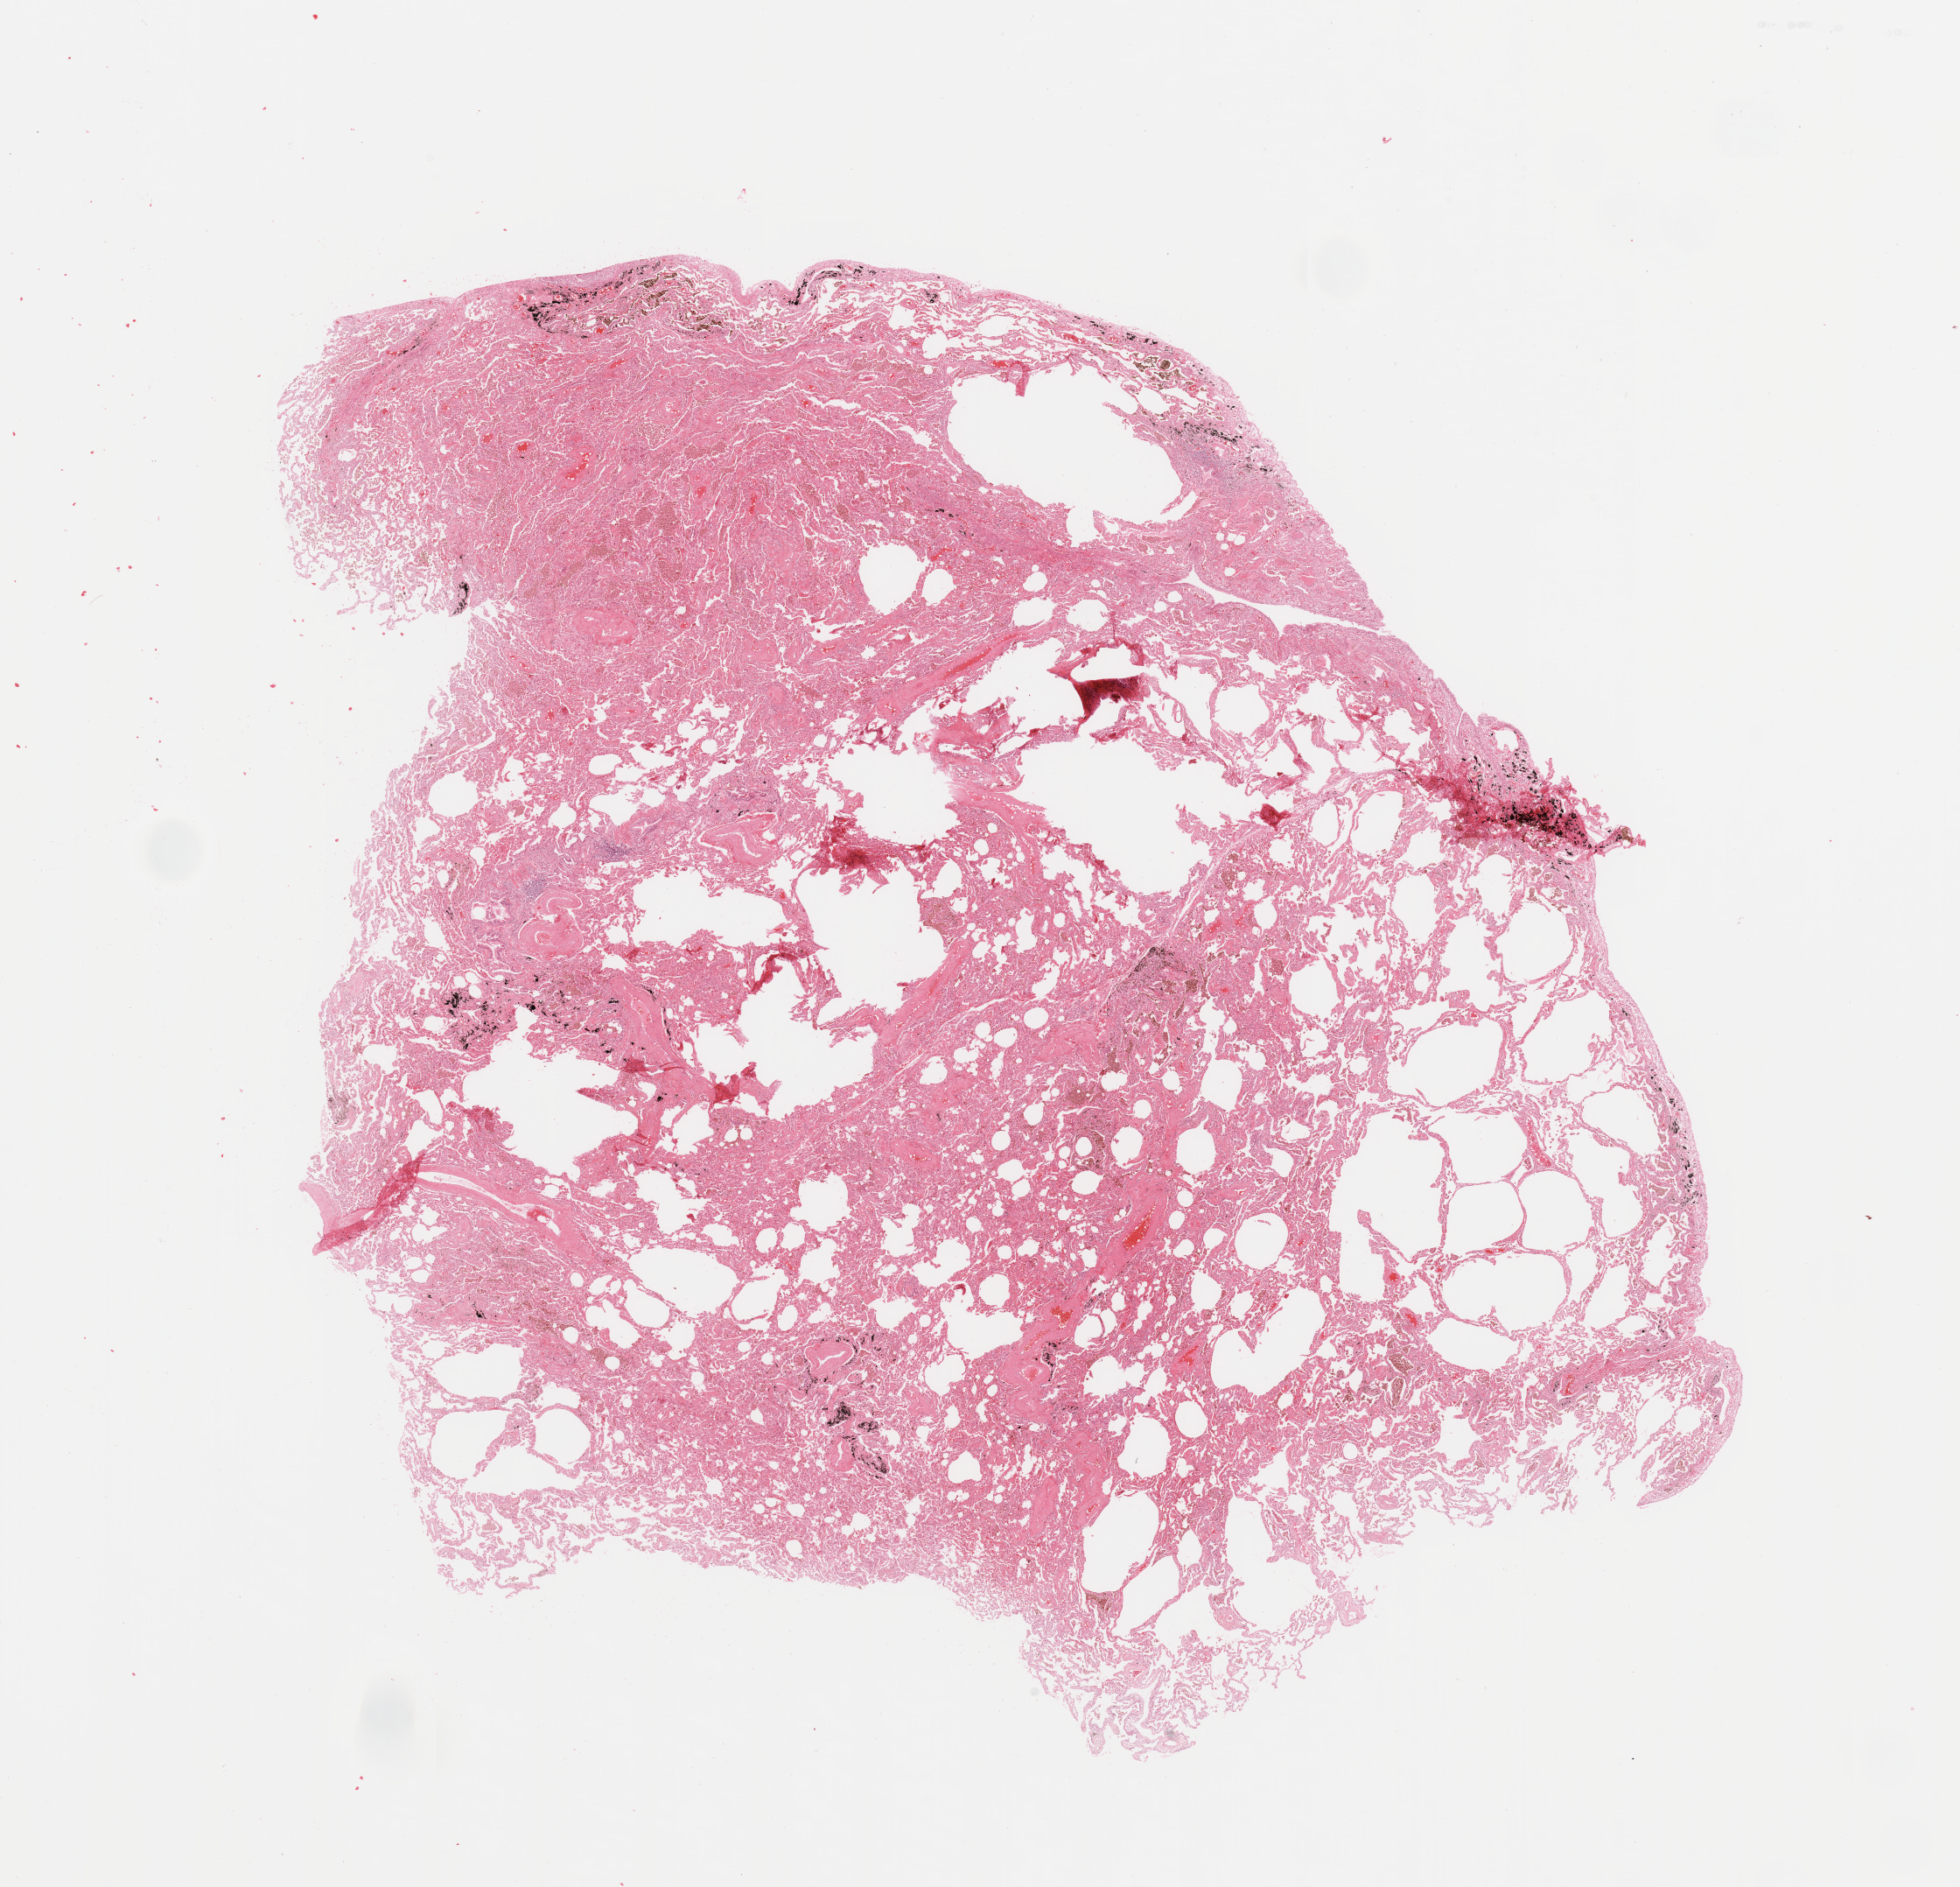
Whole-slide histology image, Hematoxylin and eosin (H&E) stained — shown as a low-resolution overview of the whole scanned area (about 17.7 x 17.1 mm, acquisition: 20x scan), lung, normal (non-tumour) tissue. Patient: male, age 59 years.
This section: normal (non-tumour) tissue from the same patient. Patient diagnosis: Squamous cell carcinoma, NOS.